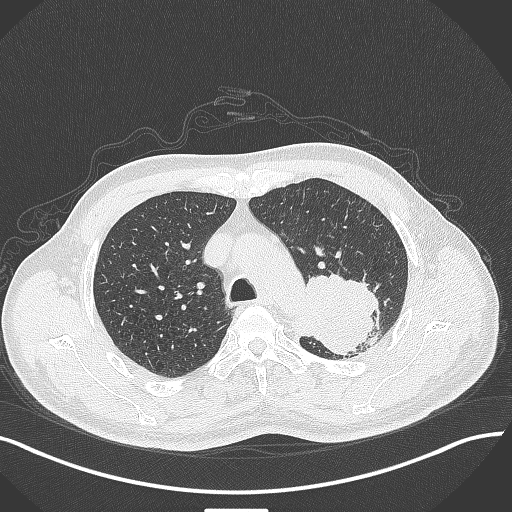
Chest CT, one axial slice; position 315 of 429 along the scan axis; reconstruction kernel B70f; 120 kVp; lung window (W 1500 / L -600 HU); 1 mm slice thickness; 512 × 512 image matrix, field of view 400 × 400 mm. Male patient, age 55 years. From the clinical record (not read from this slice): clinical TNM (as recorded): T3 N0 M1c; histopathological grade: G3.
Annotated regions visible in this slice (bounding box drawn by a radiologist):
- lung tumour (recorded histology: adenocarcinoma): bounding box (x1, y1, x2, y2) in pixels: (292, 269, 384, 362)